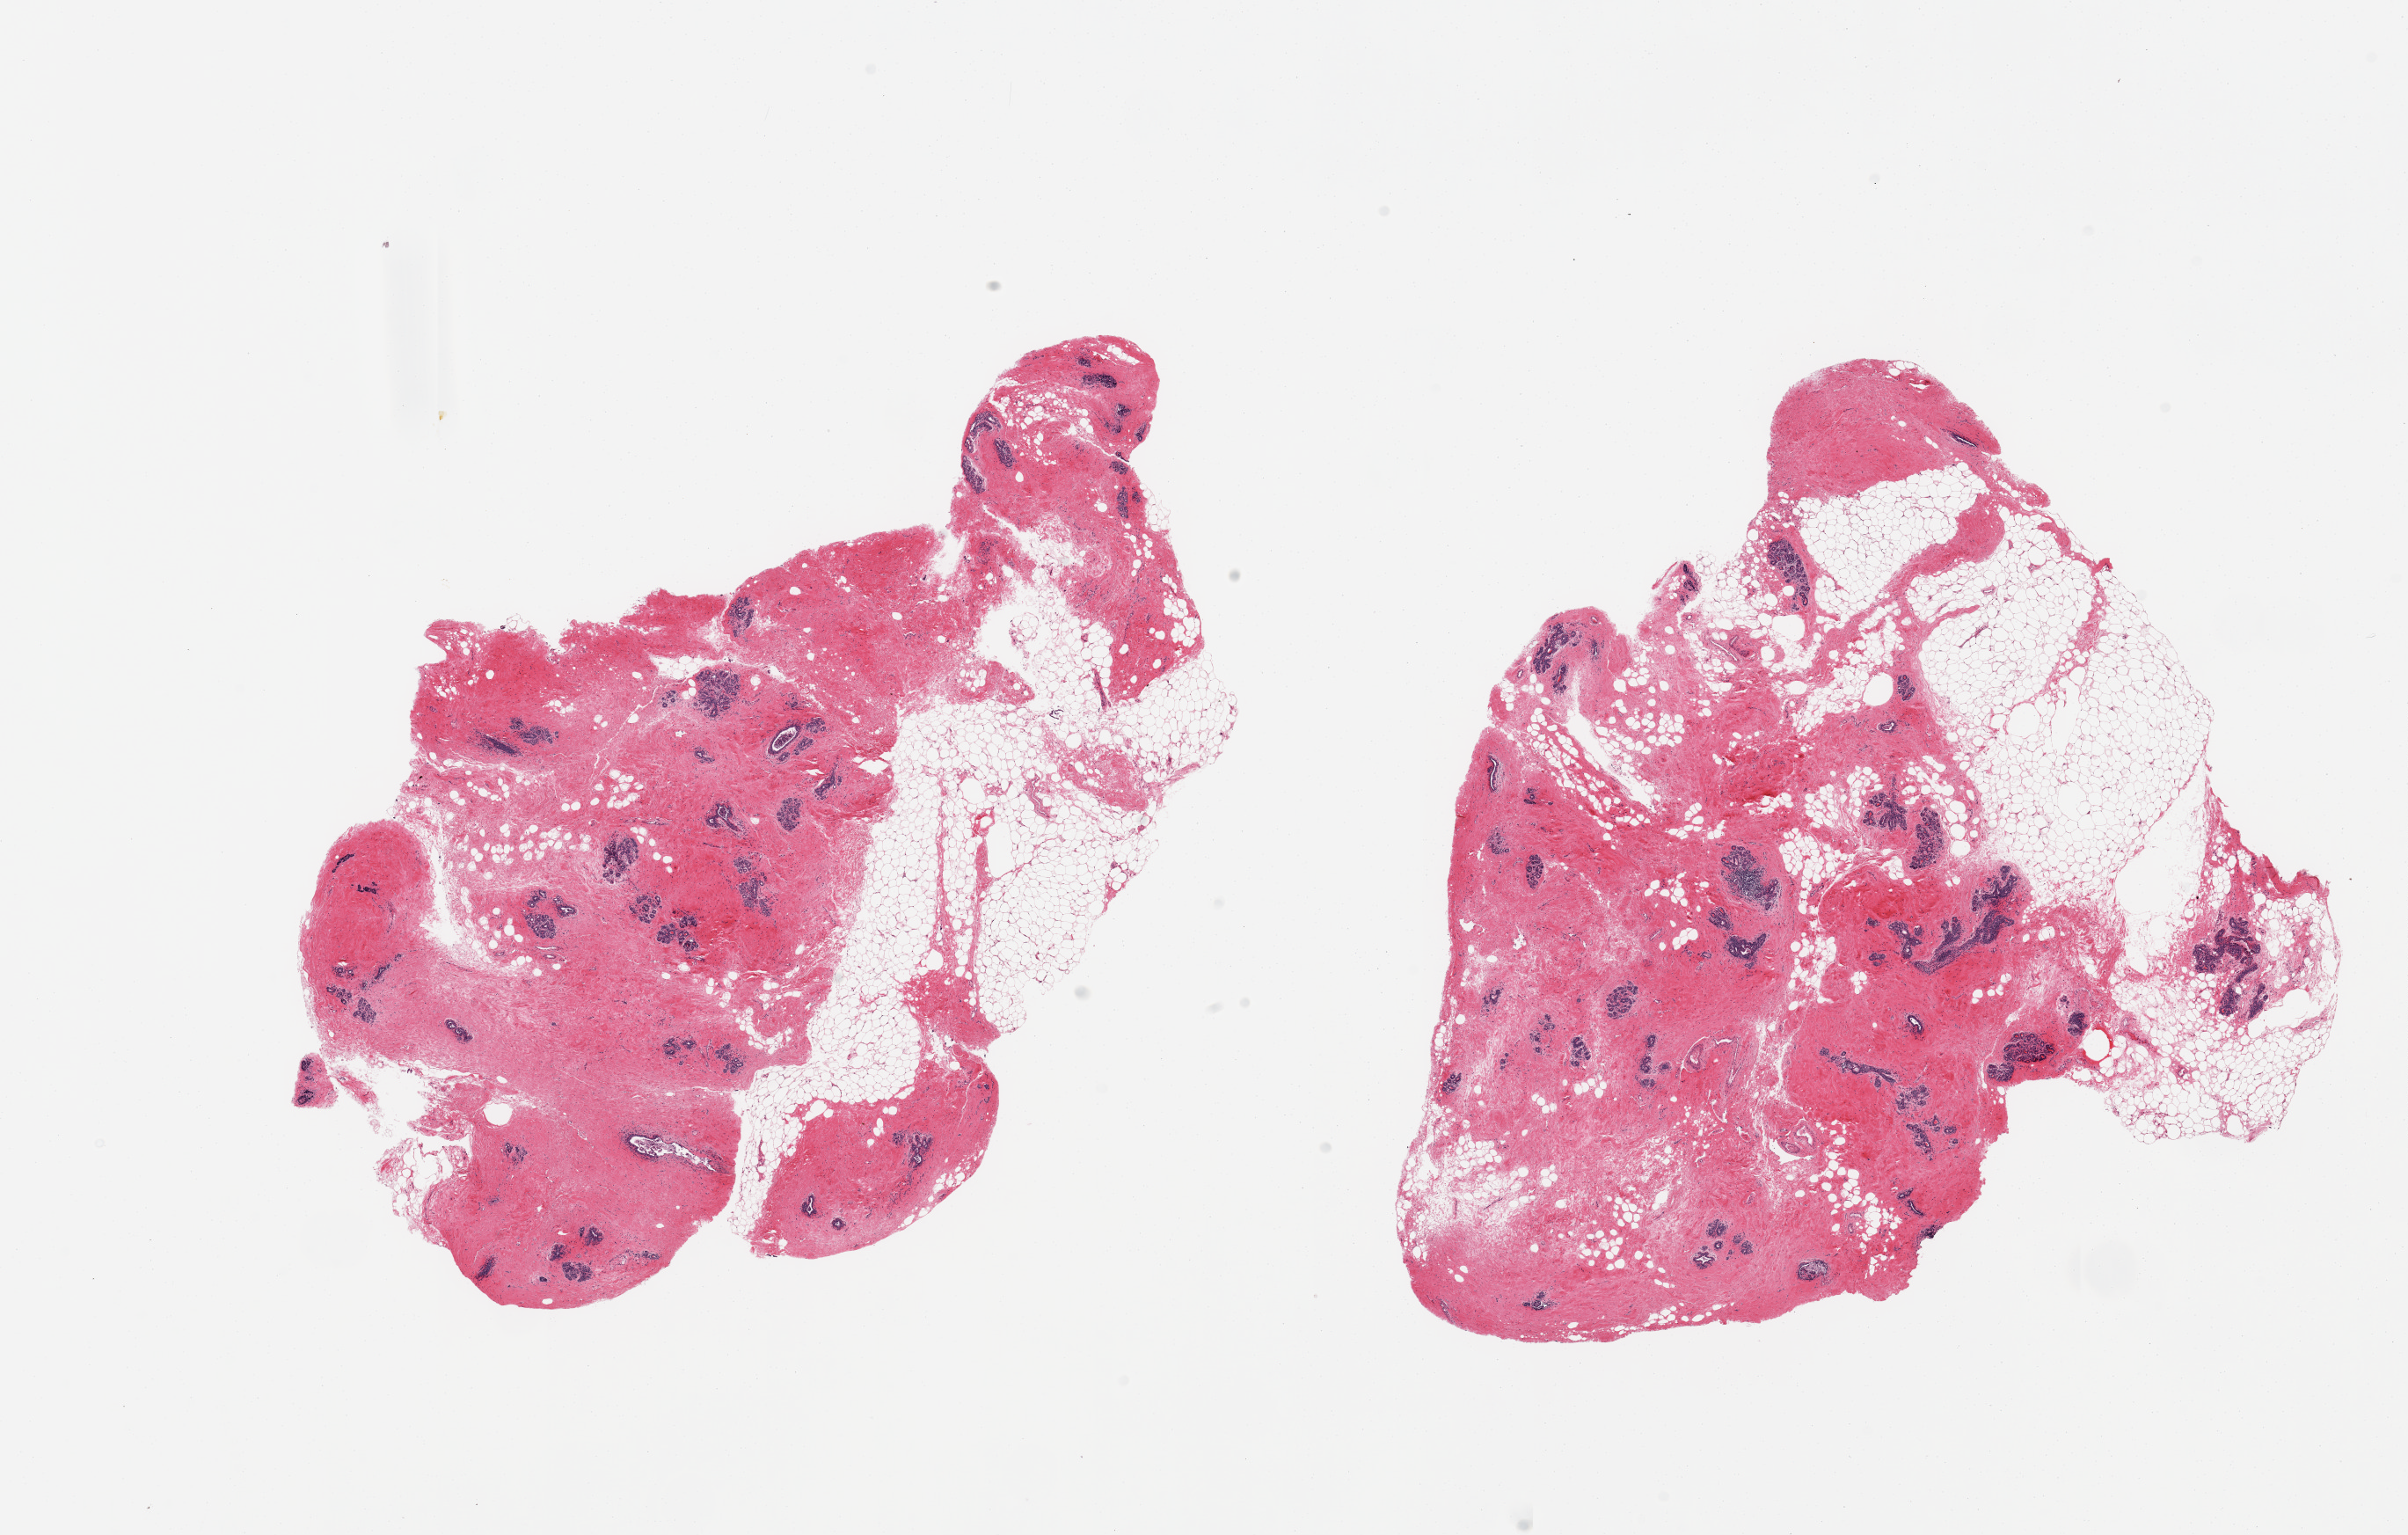
Digitized haematoxylin and eosin-stained section — low-resolution overview of the scanned area, about 21.7 x 13.8 mm, PAXgene-fixed paraffin-embedded (PFPE) section, section of breast (target tissue), tissue donor sample.
Review note (as recorded): 2 pieces, abundant ductal/lobular elements patchy chronic mastitis.